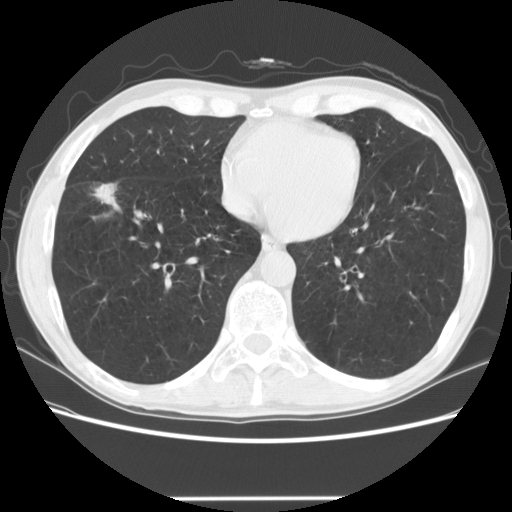
Axial slice from a low-dose chest CT screening exam. Baseline screening round. Lung window (W 1500 / L -600 HU). 2.5 mm slice thickness. Slice 92 of 145 in the series. Male, age 69 years at enrolment. Current smoker at enrolment.
Expert-annotated lung lesion, box from (x=71, y=167) to (x=131, y=219) px. The exam's reader record, not a measurement of the box and not confirmed to be the same lesion: non-calcified nodule or mass ≥4 mm, right middle lobe, 20 × 14 mm, spiculated (stellate) margins, mixed attenuation. Official screen result: positive, change unspecified: nodule(s) >= 4 mm or enlarging nodule(s), mass(es), or other non-specific abnormalities suspicious for lung cancer. Participant outcome: lung cancer diagnosed 86 days after this screen — squamous cell carcinoma, NOS, right middle lobe, poorly differentiated (G3), stage IA (AJCC 6th edition), 15 mm at pathology.